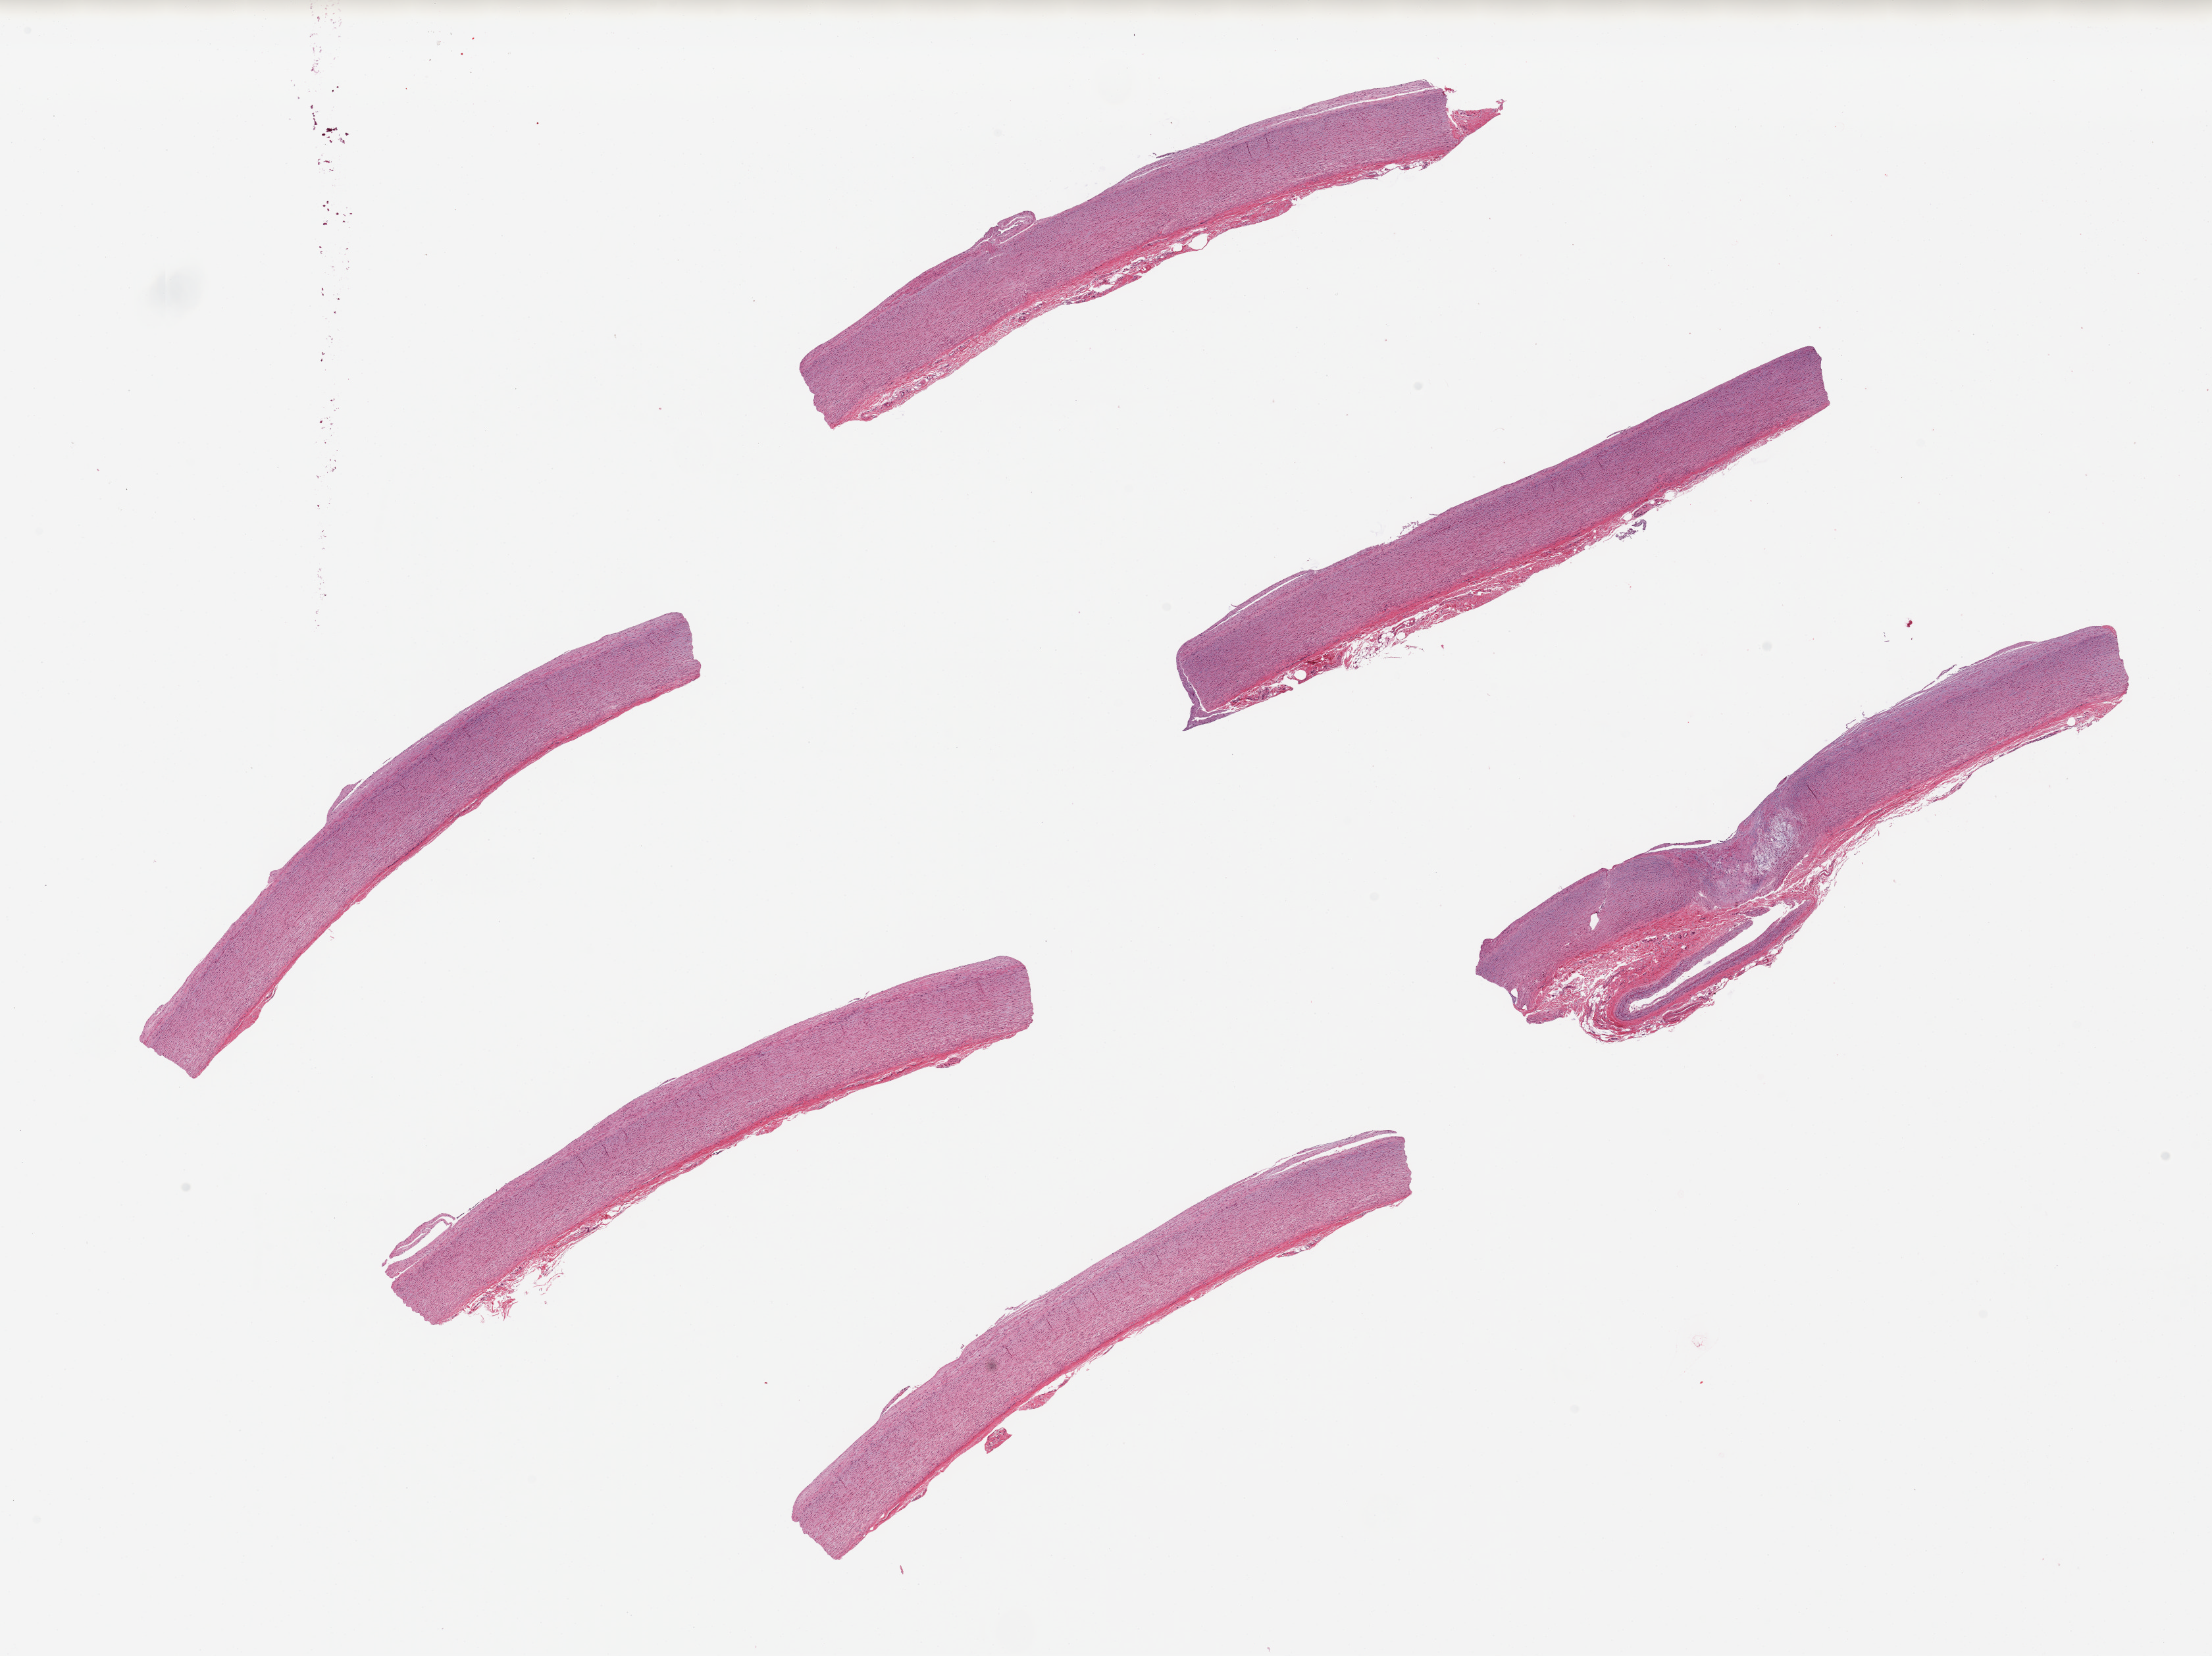
Digitized haematoxylin and eosin-stained section, brightfield — a low-resolution overview of the entire scanned area, about 26.6 x 19.9 mm (slide scanned at 20x); PAXgene-fixed paraffin-embedded (PFPE) section; target tissue: aorta; donor tissue sample. Female donor.
Pathologist's review note for this sample: 6 pieces. 8x1.5mm. focal fatty deposit.